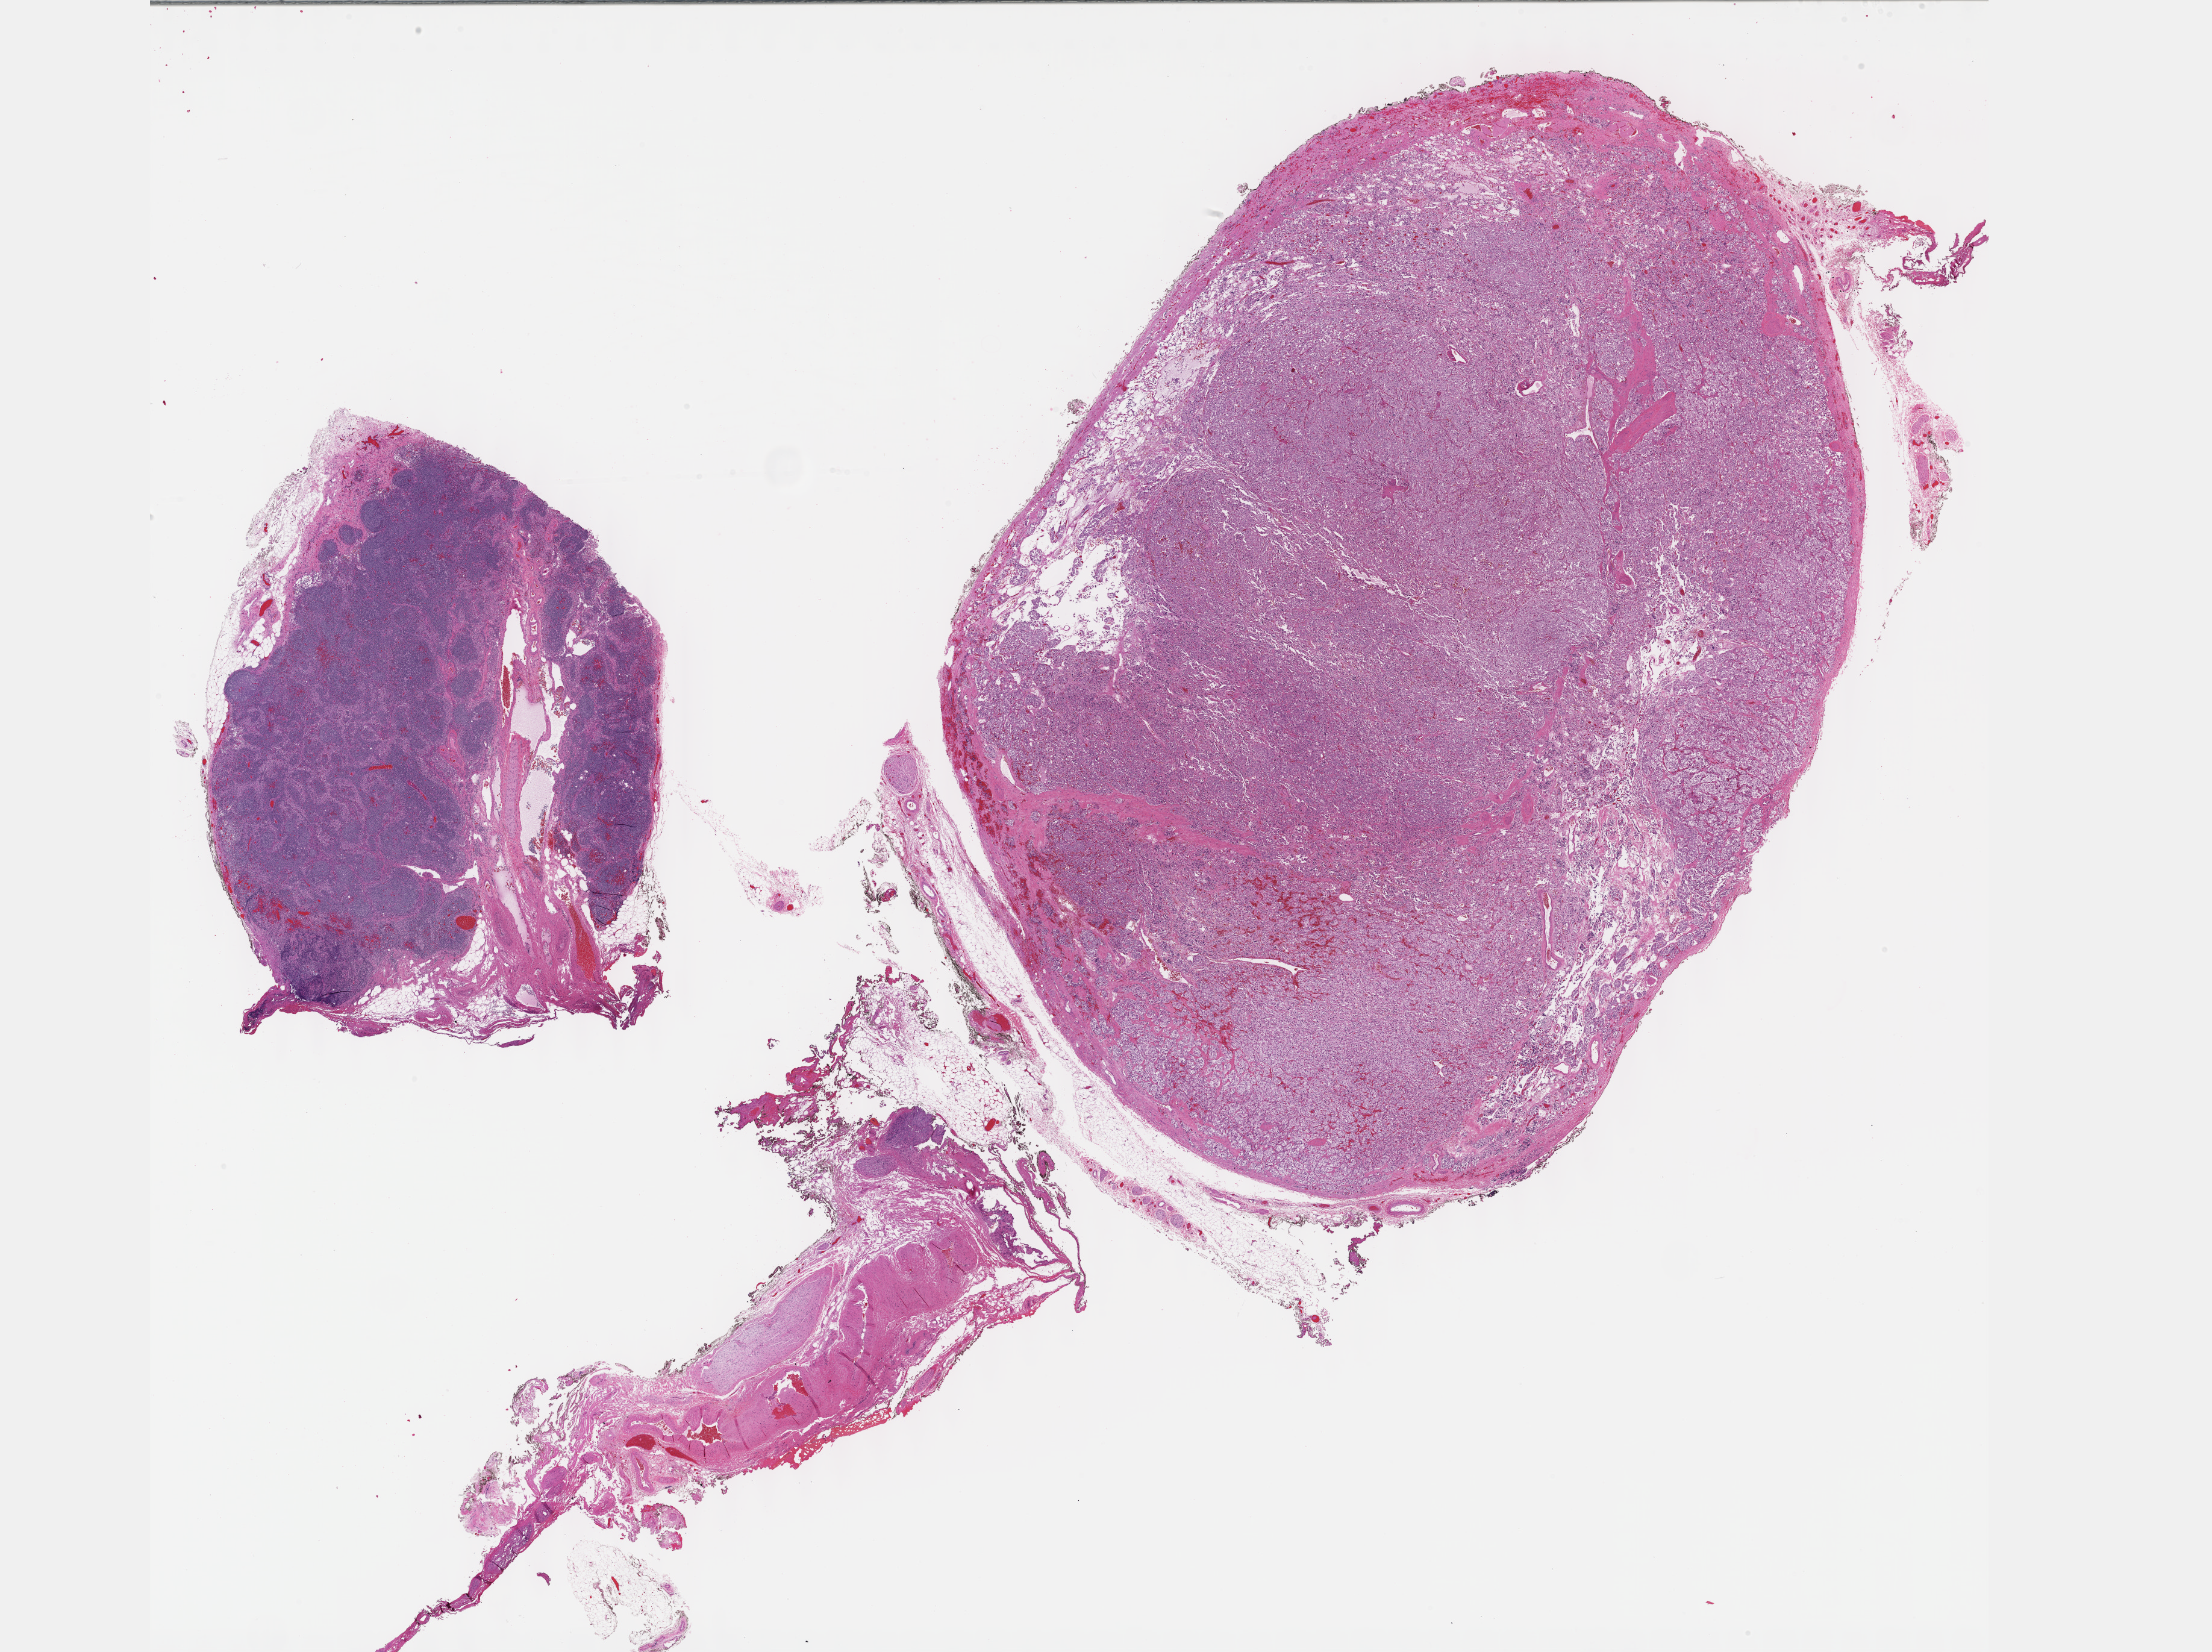
Whole-slide histology image, H&E — shown as a low-resolution overview of the whole scanned area (about 29.7 x 22.2 mm, from a 40x scan); FFPE section; primary tumour sample from the connective, subcutaneous and other soft tissues. Female patient; age at initial diagnosis 39 years.
Pathologic diagnosis: Aortic body tumor (connective, subcutaneous and other soft tissues of thorax). Lymph nodes positive (case pathology): 0 of 10 examined.